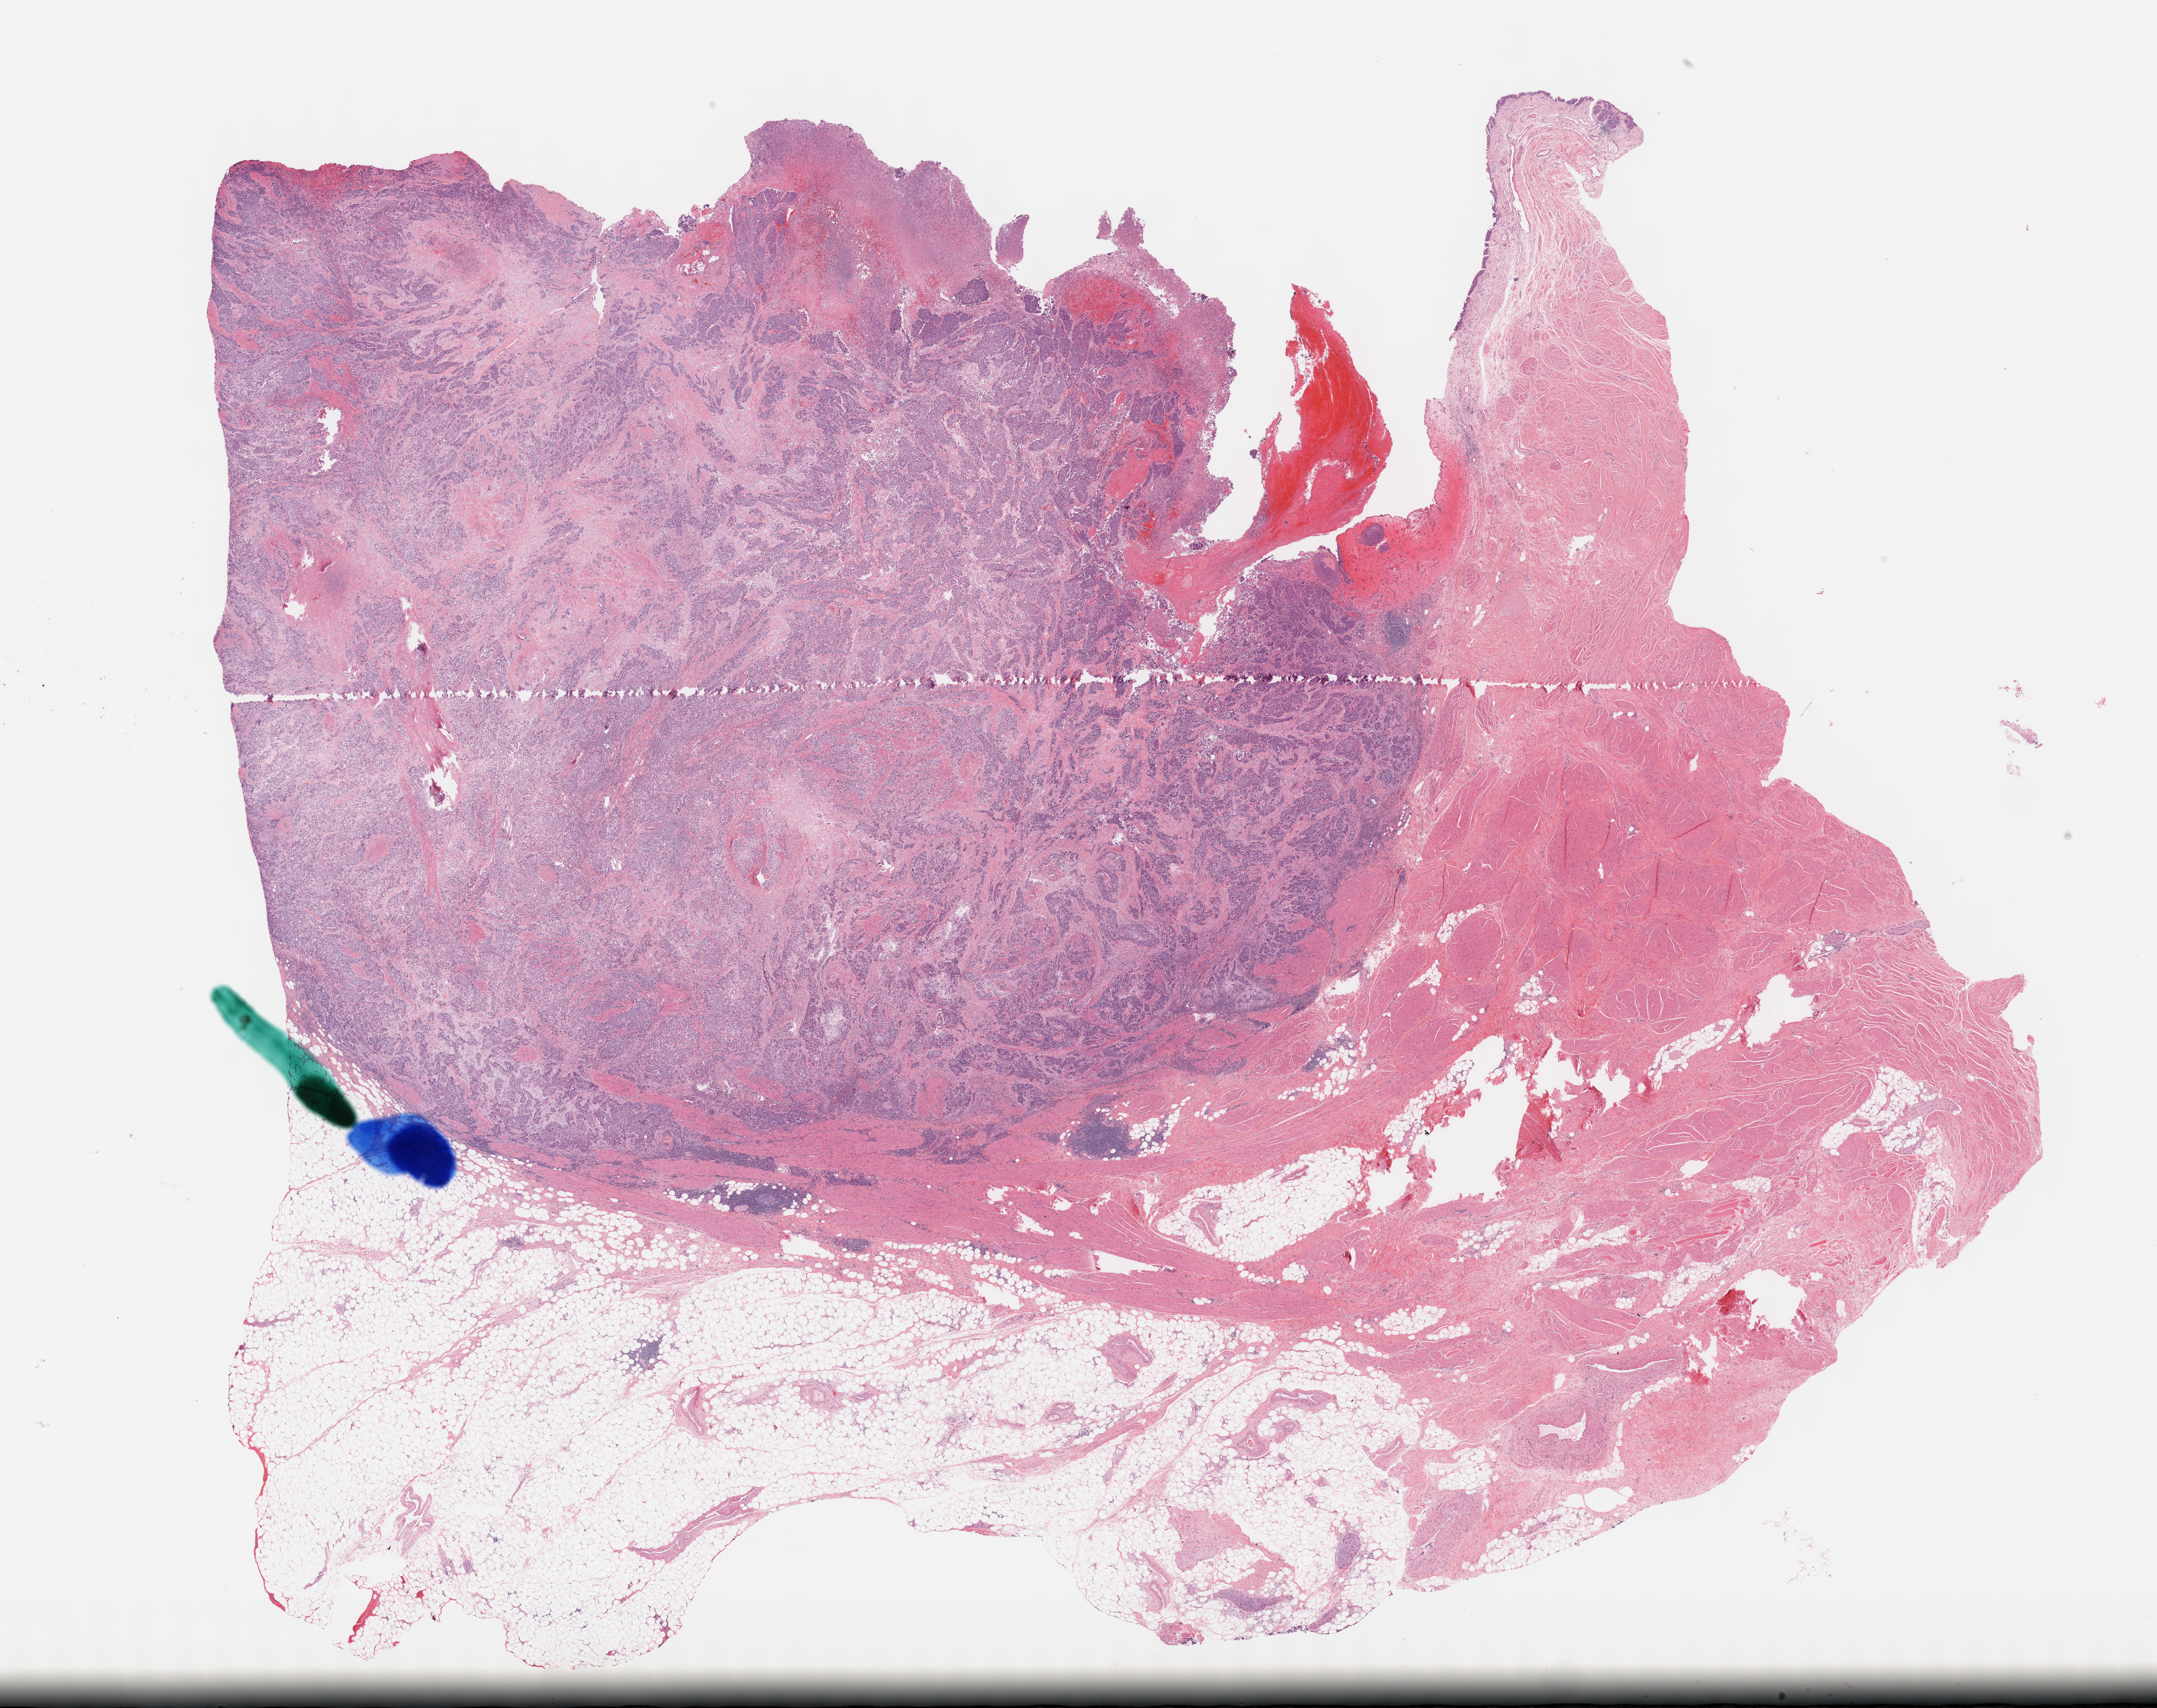
Hematoxylin and eosin (H&E) stained whole-slide image, a low-resolution overview of the entire scanned area, about 26.7 x 21.1 mm. Formalin-fixed paraffin-embedded (FFPE) diagnostic section. Bladder, primary tumour sample. Patient: male, age at initial diagnosis 80 years. Histologic grade: high grade.
• AJCC pathologic stage: III (7th edition)
• TNM: T3a N0 MX
• diagnosis: Transitional cell carcinoma (anterior wall of bladder)